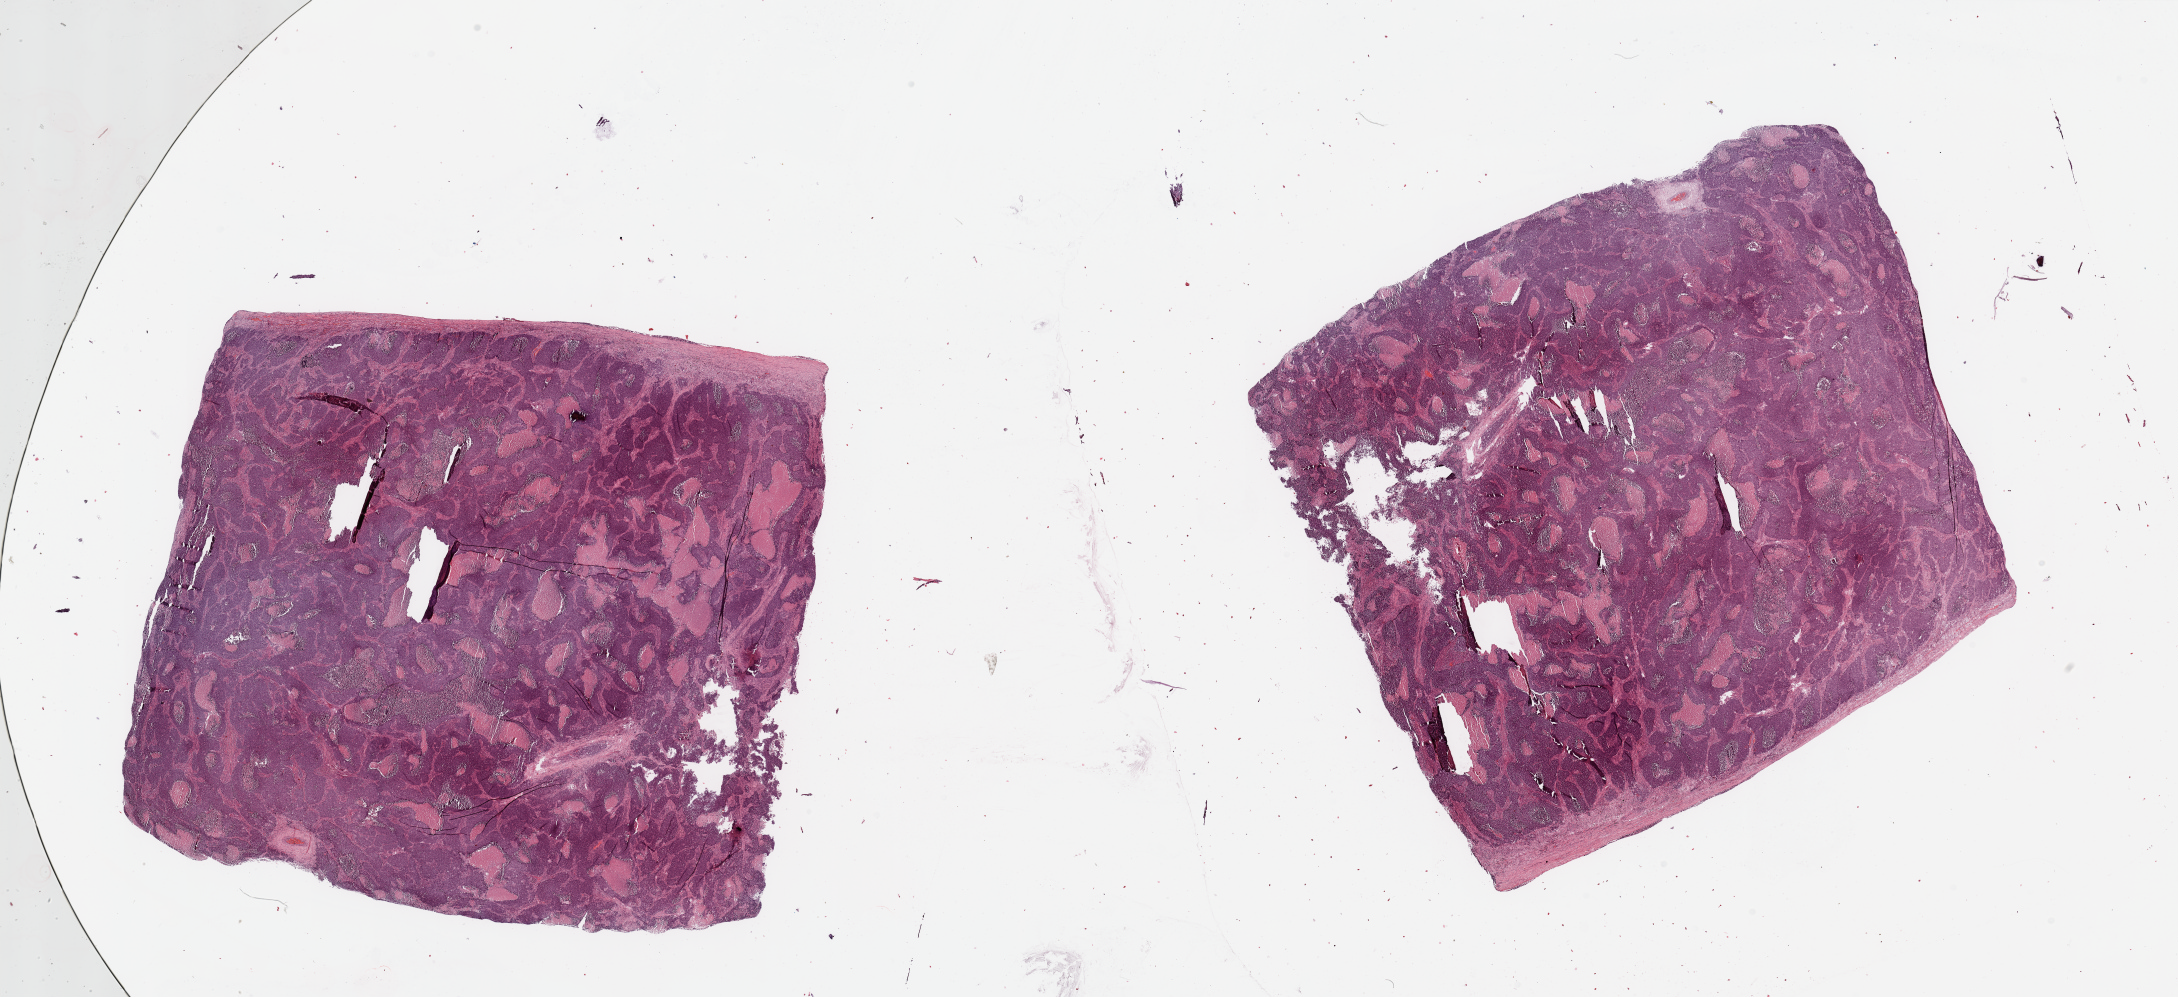
H&E-stained whole-slide image — whole scanned area (about 34.5 x 15.8 mm) shown as a low-resolution overview; lung, tumour tissue. 61-year-old male patient. Histologic grade: G3 (poorly differentiated).
- histologic diagnosis: Squamous cell carcinoma, NOS
- AJCC pathologic stage: IIB